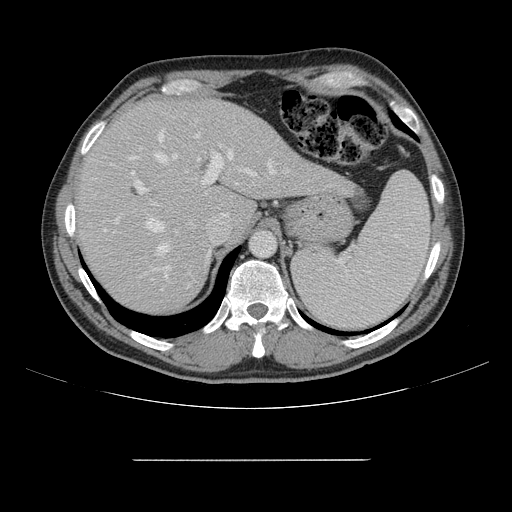
Contrast-enhanced abdominal CT, one axial slice; position 114 of 164 along the scan axis; intravenous contrast given; soft-tissue window (W 400 / L 40 HU); 512 × 512 image matrix, field of view 404 × 404 mm. Male patient, age 54 years. From the clinical record (not read from this slice): diagnosis: colorectal cancer liver metastases, imaged before liver resection; multiple liver metastases: yes.
Annotated regions visible in this slice (manually delineated by an expert):
- hepatic veins: box from (x=147, y=133) to (x=288, y=280) px
- liver: (x=77, y=100)–(x=344, y=313)
- planned liver remnant (the part of the liver to remain after resection): (x=77, y=100)–(x=246, y=313)
- portal vein (with intrahepatic branches): (x=116, y=129)–(x=255, y=291)